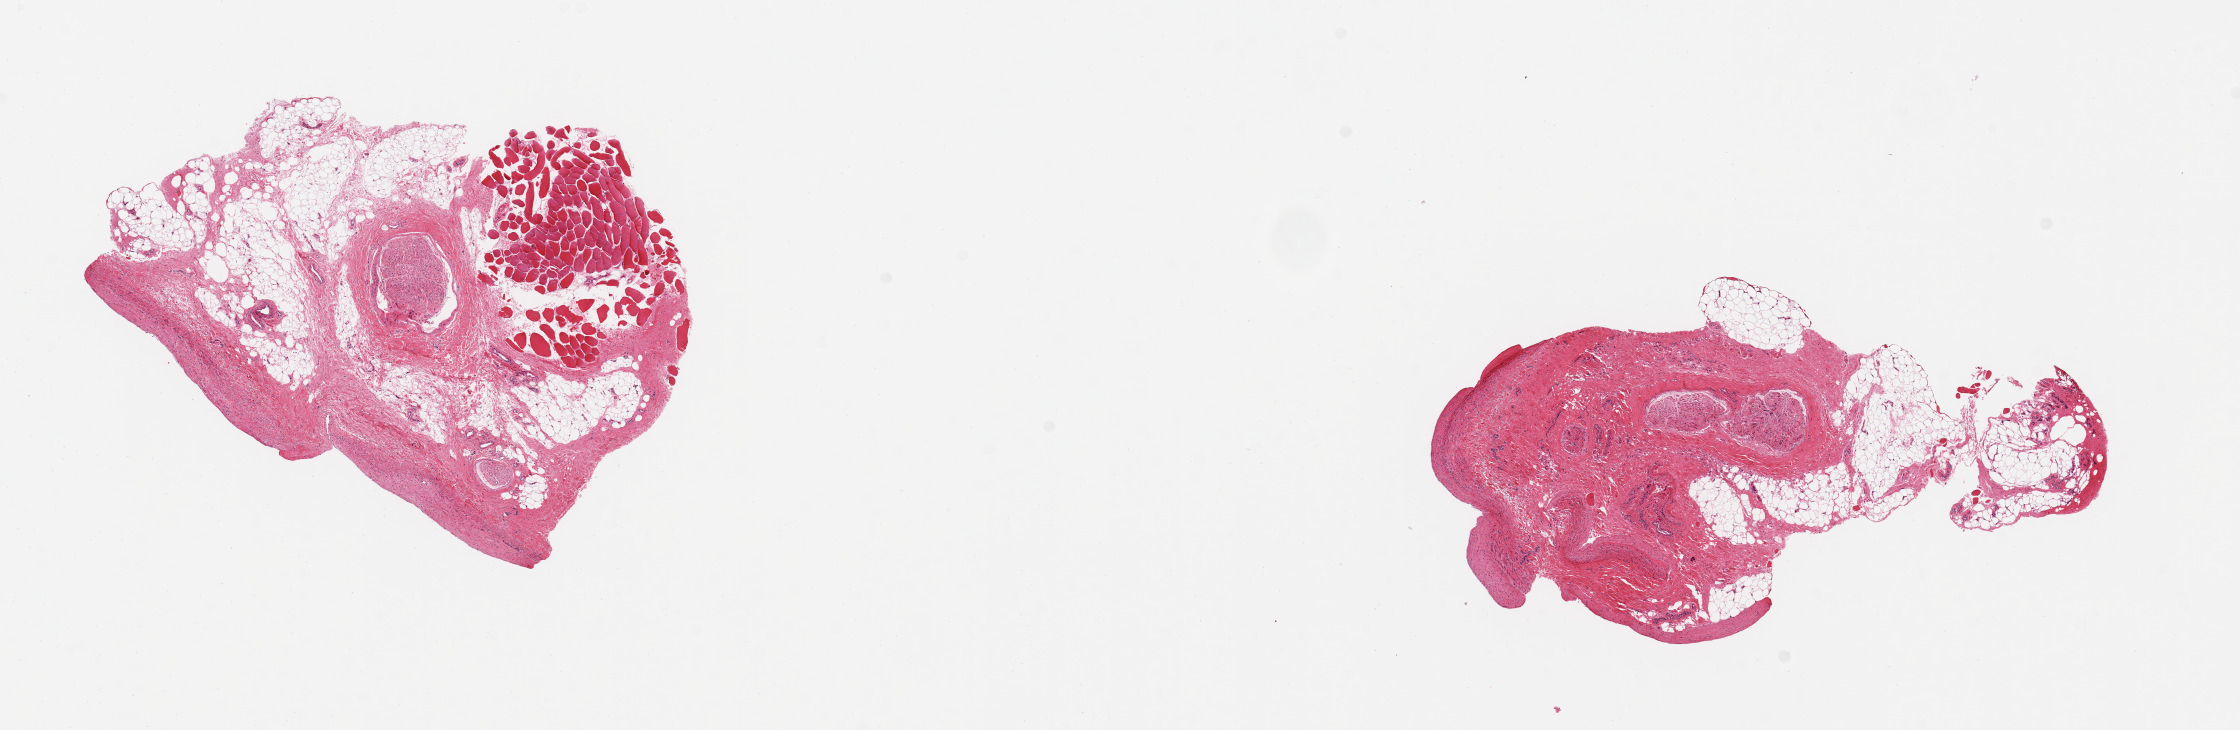
Digitized haematoxylin and eosin-stained section, low-resolution overview of the scanned area, about 17.7 x 5.8 mm. PAXgene-fixed, paraffin-embedded tissue. Section of tibial artery (target tissue). Donor tissue sample.
Pathologist's review note for this sample: 2 pieces; each has 75% nerve, fat, & muscle.